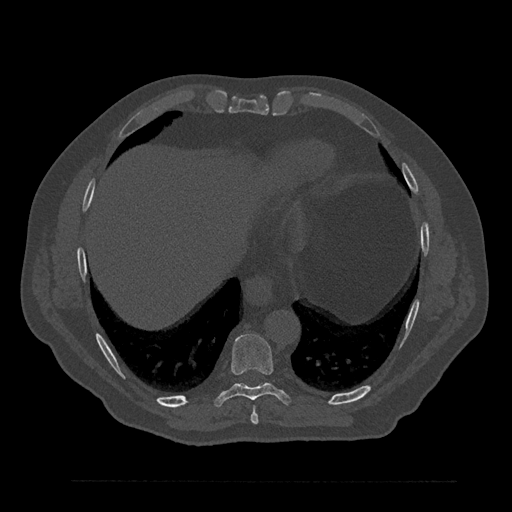
CT including the spine, one axial slice. Position 403 of 797 along the scan axis. Bone window (W 1800 / L 400 HU). 0.5 mm slice thickness. 512 × 512 image matrix, field of view 430 × 430 mm. Male patient, age 61 years. From the clinical record (not read from this slice): primary cancer: prostate.
Annotated regions visible in this slice (semi-automatic segmentation, software-assisted and operator-edited):
- T8 vertebra: bounding box (x1, y1, x2, y2) in pixels: (251, 407, 259, 425)
- T9 vertebra: (214, 333, 290, 407)